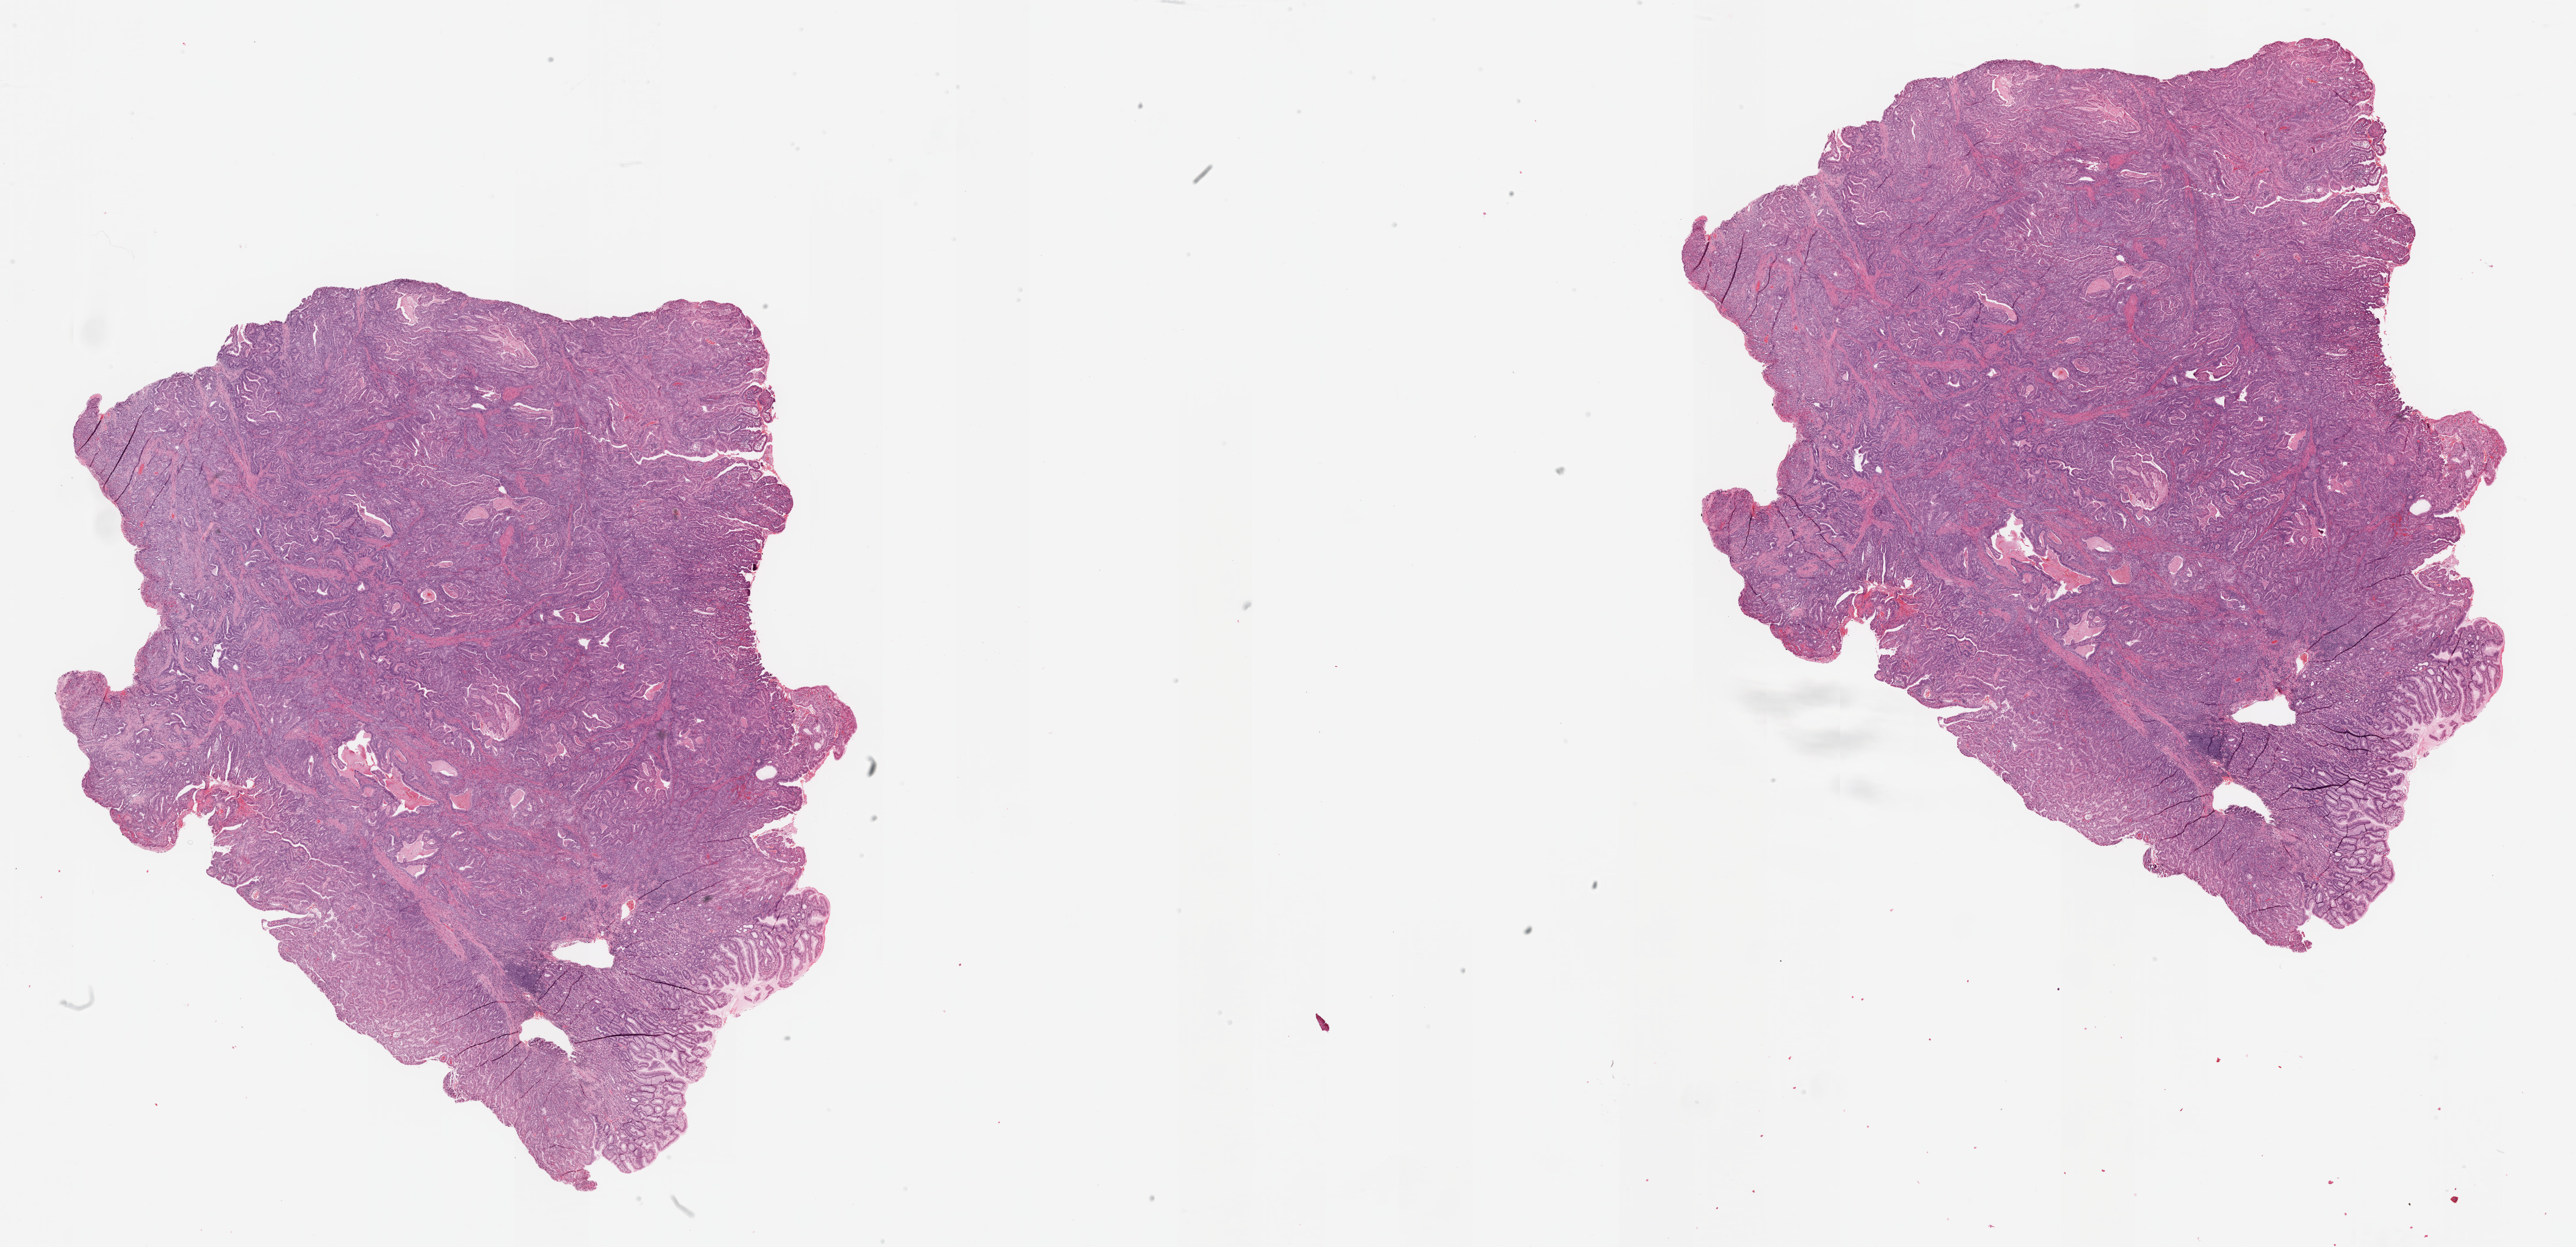
Whole-slide histology image, Hematoxylin and eosin (H&E) stained, low-resolution overview of the scanned area, about 35.0 x 17.0 mm (slide scanned at 20x); formalin-fixed paraffin-embedded (FFPE) diagnostic section; stomach, primary tumour sample. Female patient. Histologic grade: G2 (moderately differentiated).
- AJCC pathologic stage: IB (6th edition)
- pathologic diagnosis: Adenocarcinoma, NOS